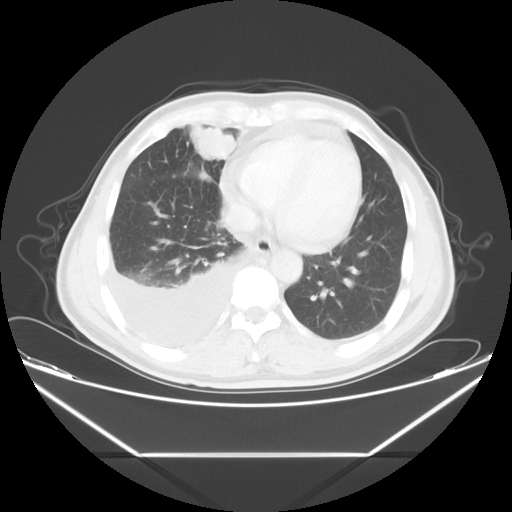
Chest CT, one axial slice; slice 17 of 56 in the series (ordered by position); reconstruction kernel STANDARD; 120 kVp; lung window (W 1500 / L -600 HU); 5 mm slice thickness; 512 × 512 image matrix, field of view 412 × 412 mm. Male patient, age 57 years. Case-level facts recorded for this patient, not image findings: clinical TNM (as recorded): T2 N3 M1.
Annotated regions visible in this slice (bounding box drawn by a radiologist):
- lung tumour (recorded histology: adenocarcinoma): bounding box [x1, y1, x2, y2] px = [188, 118, 237, 162]